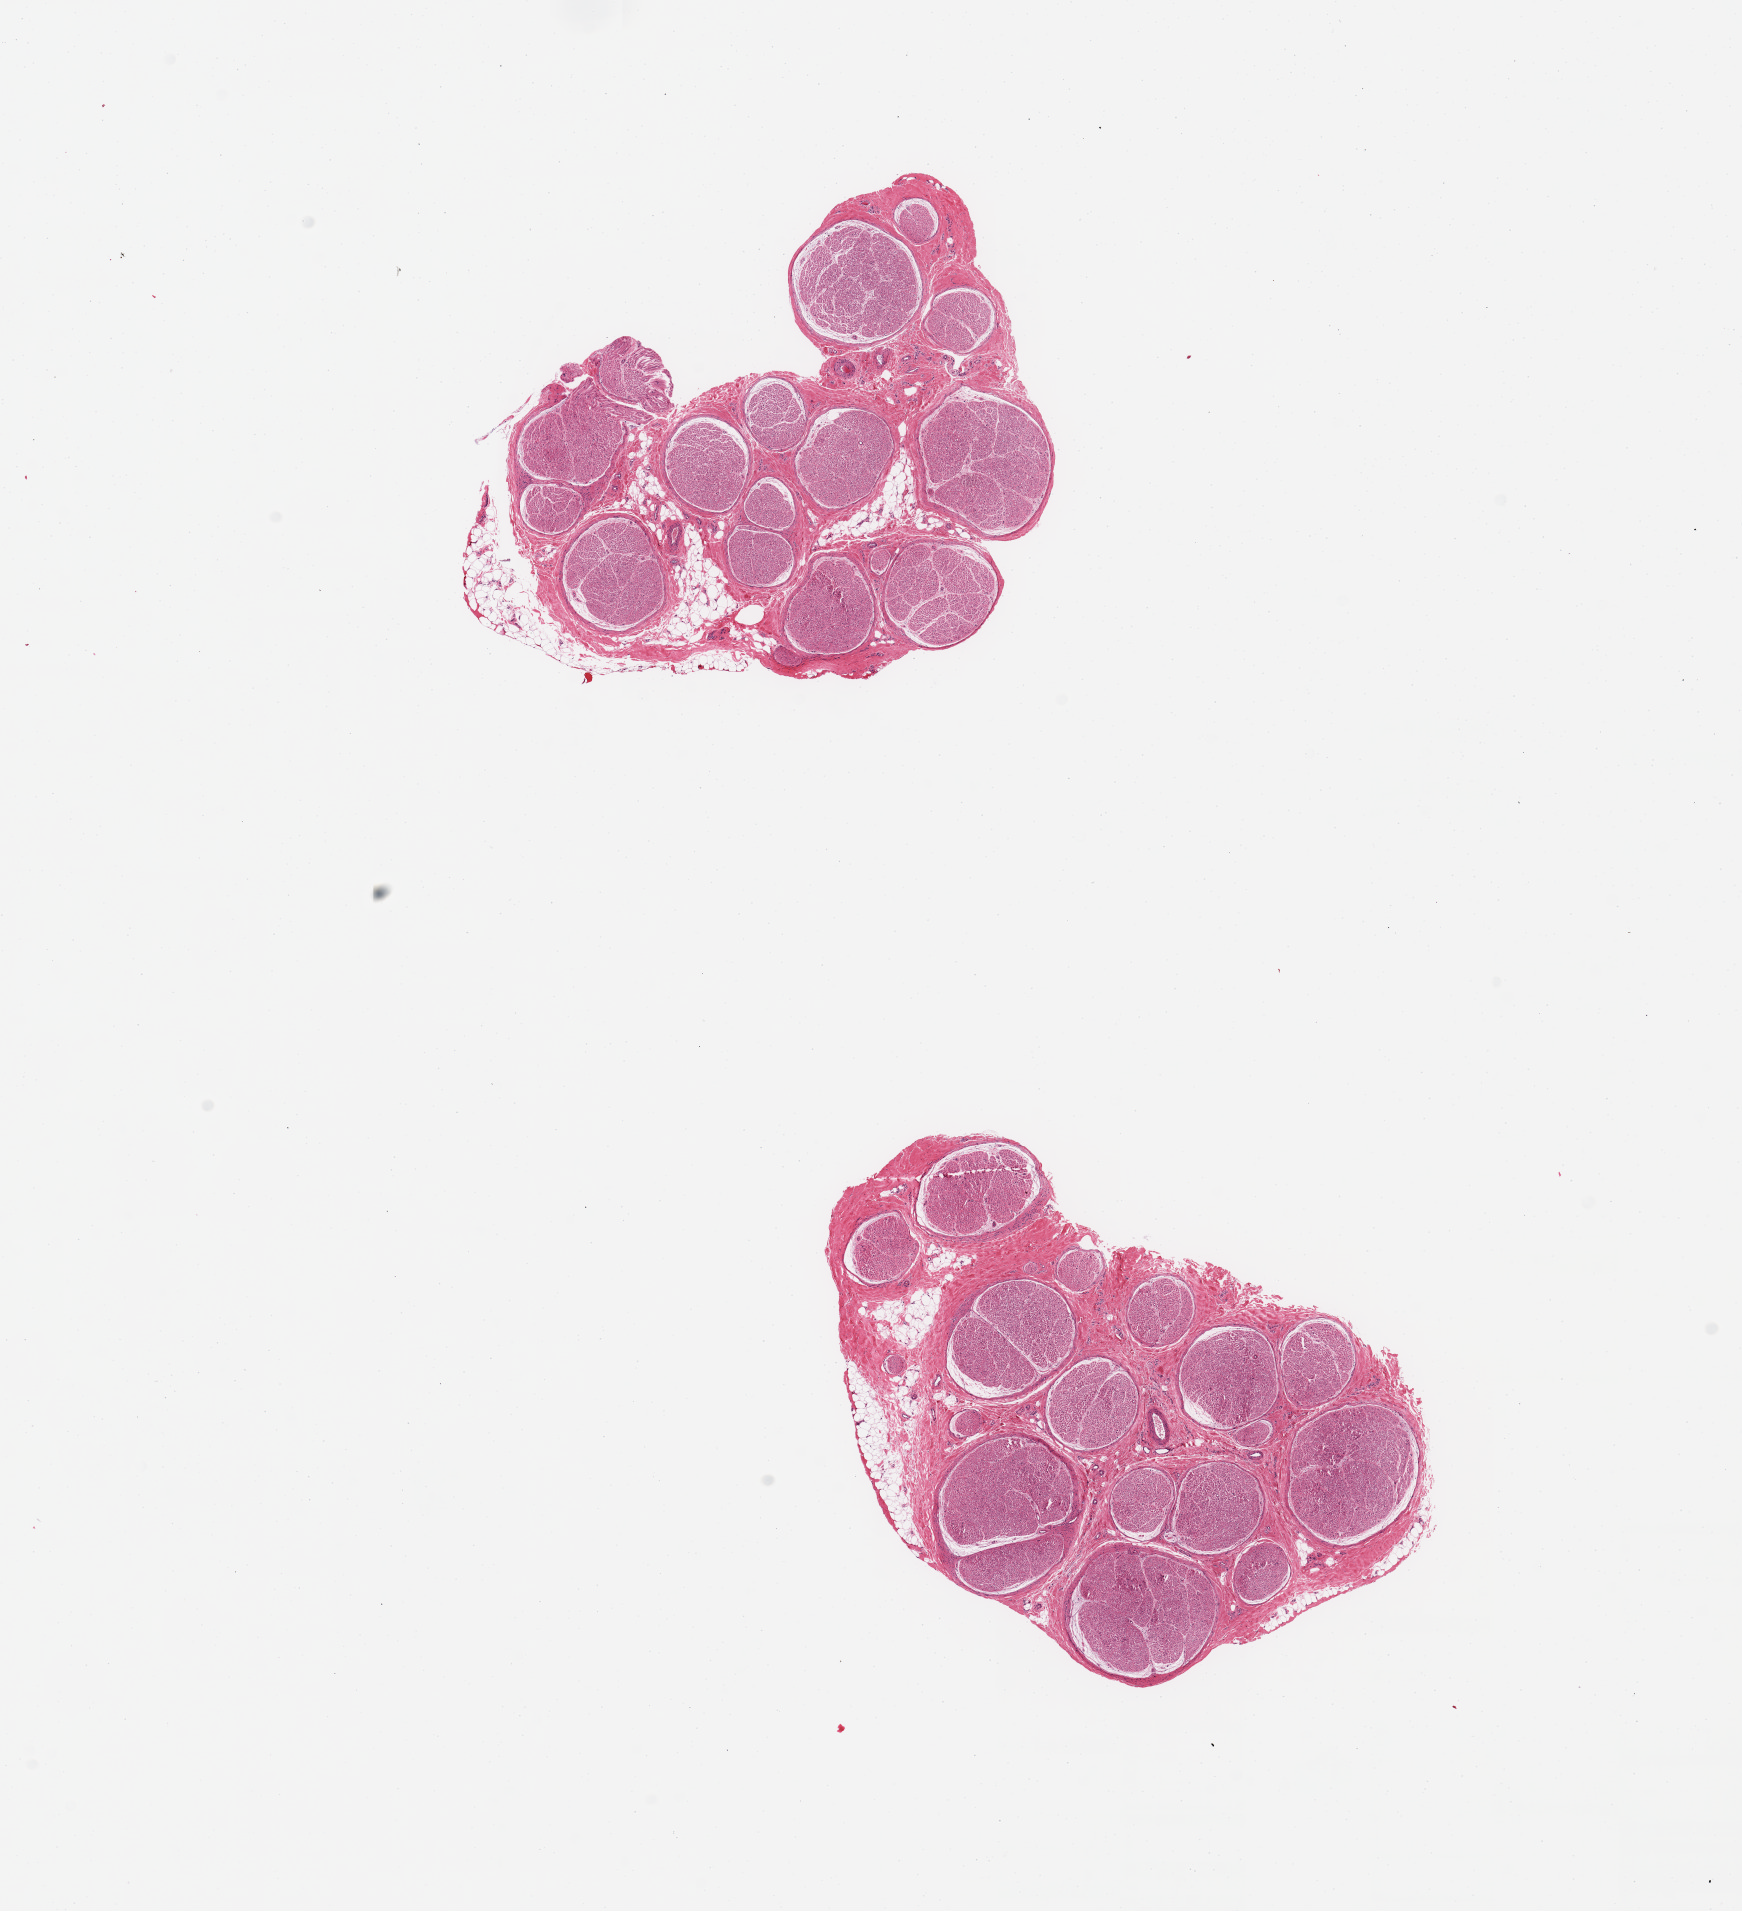
Digitized hematoxylin and eosin (H&E)-stained section — shown as a low-resolution overview of the whole scanned area (about 13.8 x 15.1 mm, slide scanned at 20x). PAXgene-fixed paraffin-embedded (PFPE) section. Section of tibial nerve (target tissue). Tissue donor sample. Donor: male.
• pathologist's review note for this sample: 2 pieces; ~10% internal/external fat